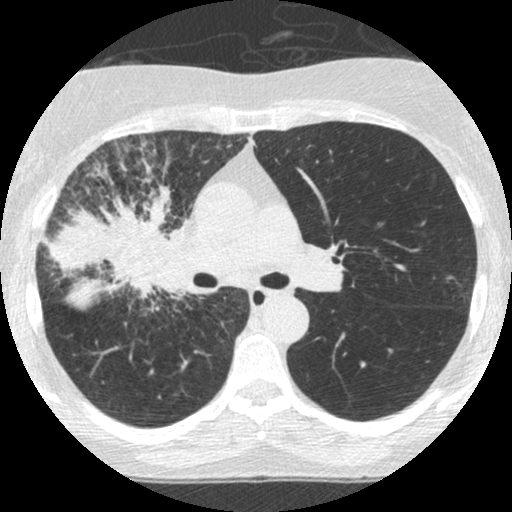
Low-dose screening chest CT, one axial slice. Position 159 of 253 along the scan axis. 120 kVp. Lung window (W 1500 / L -600 HU). 512 × 512 image matrix.
Structures marked on this image (manually delineated by an expert):
- lesion 2 (tumor, hilum of right lung): bounding box (x1, y1, x2, y2) in pixels: (45, 185, 184, 312)